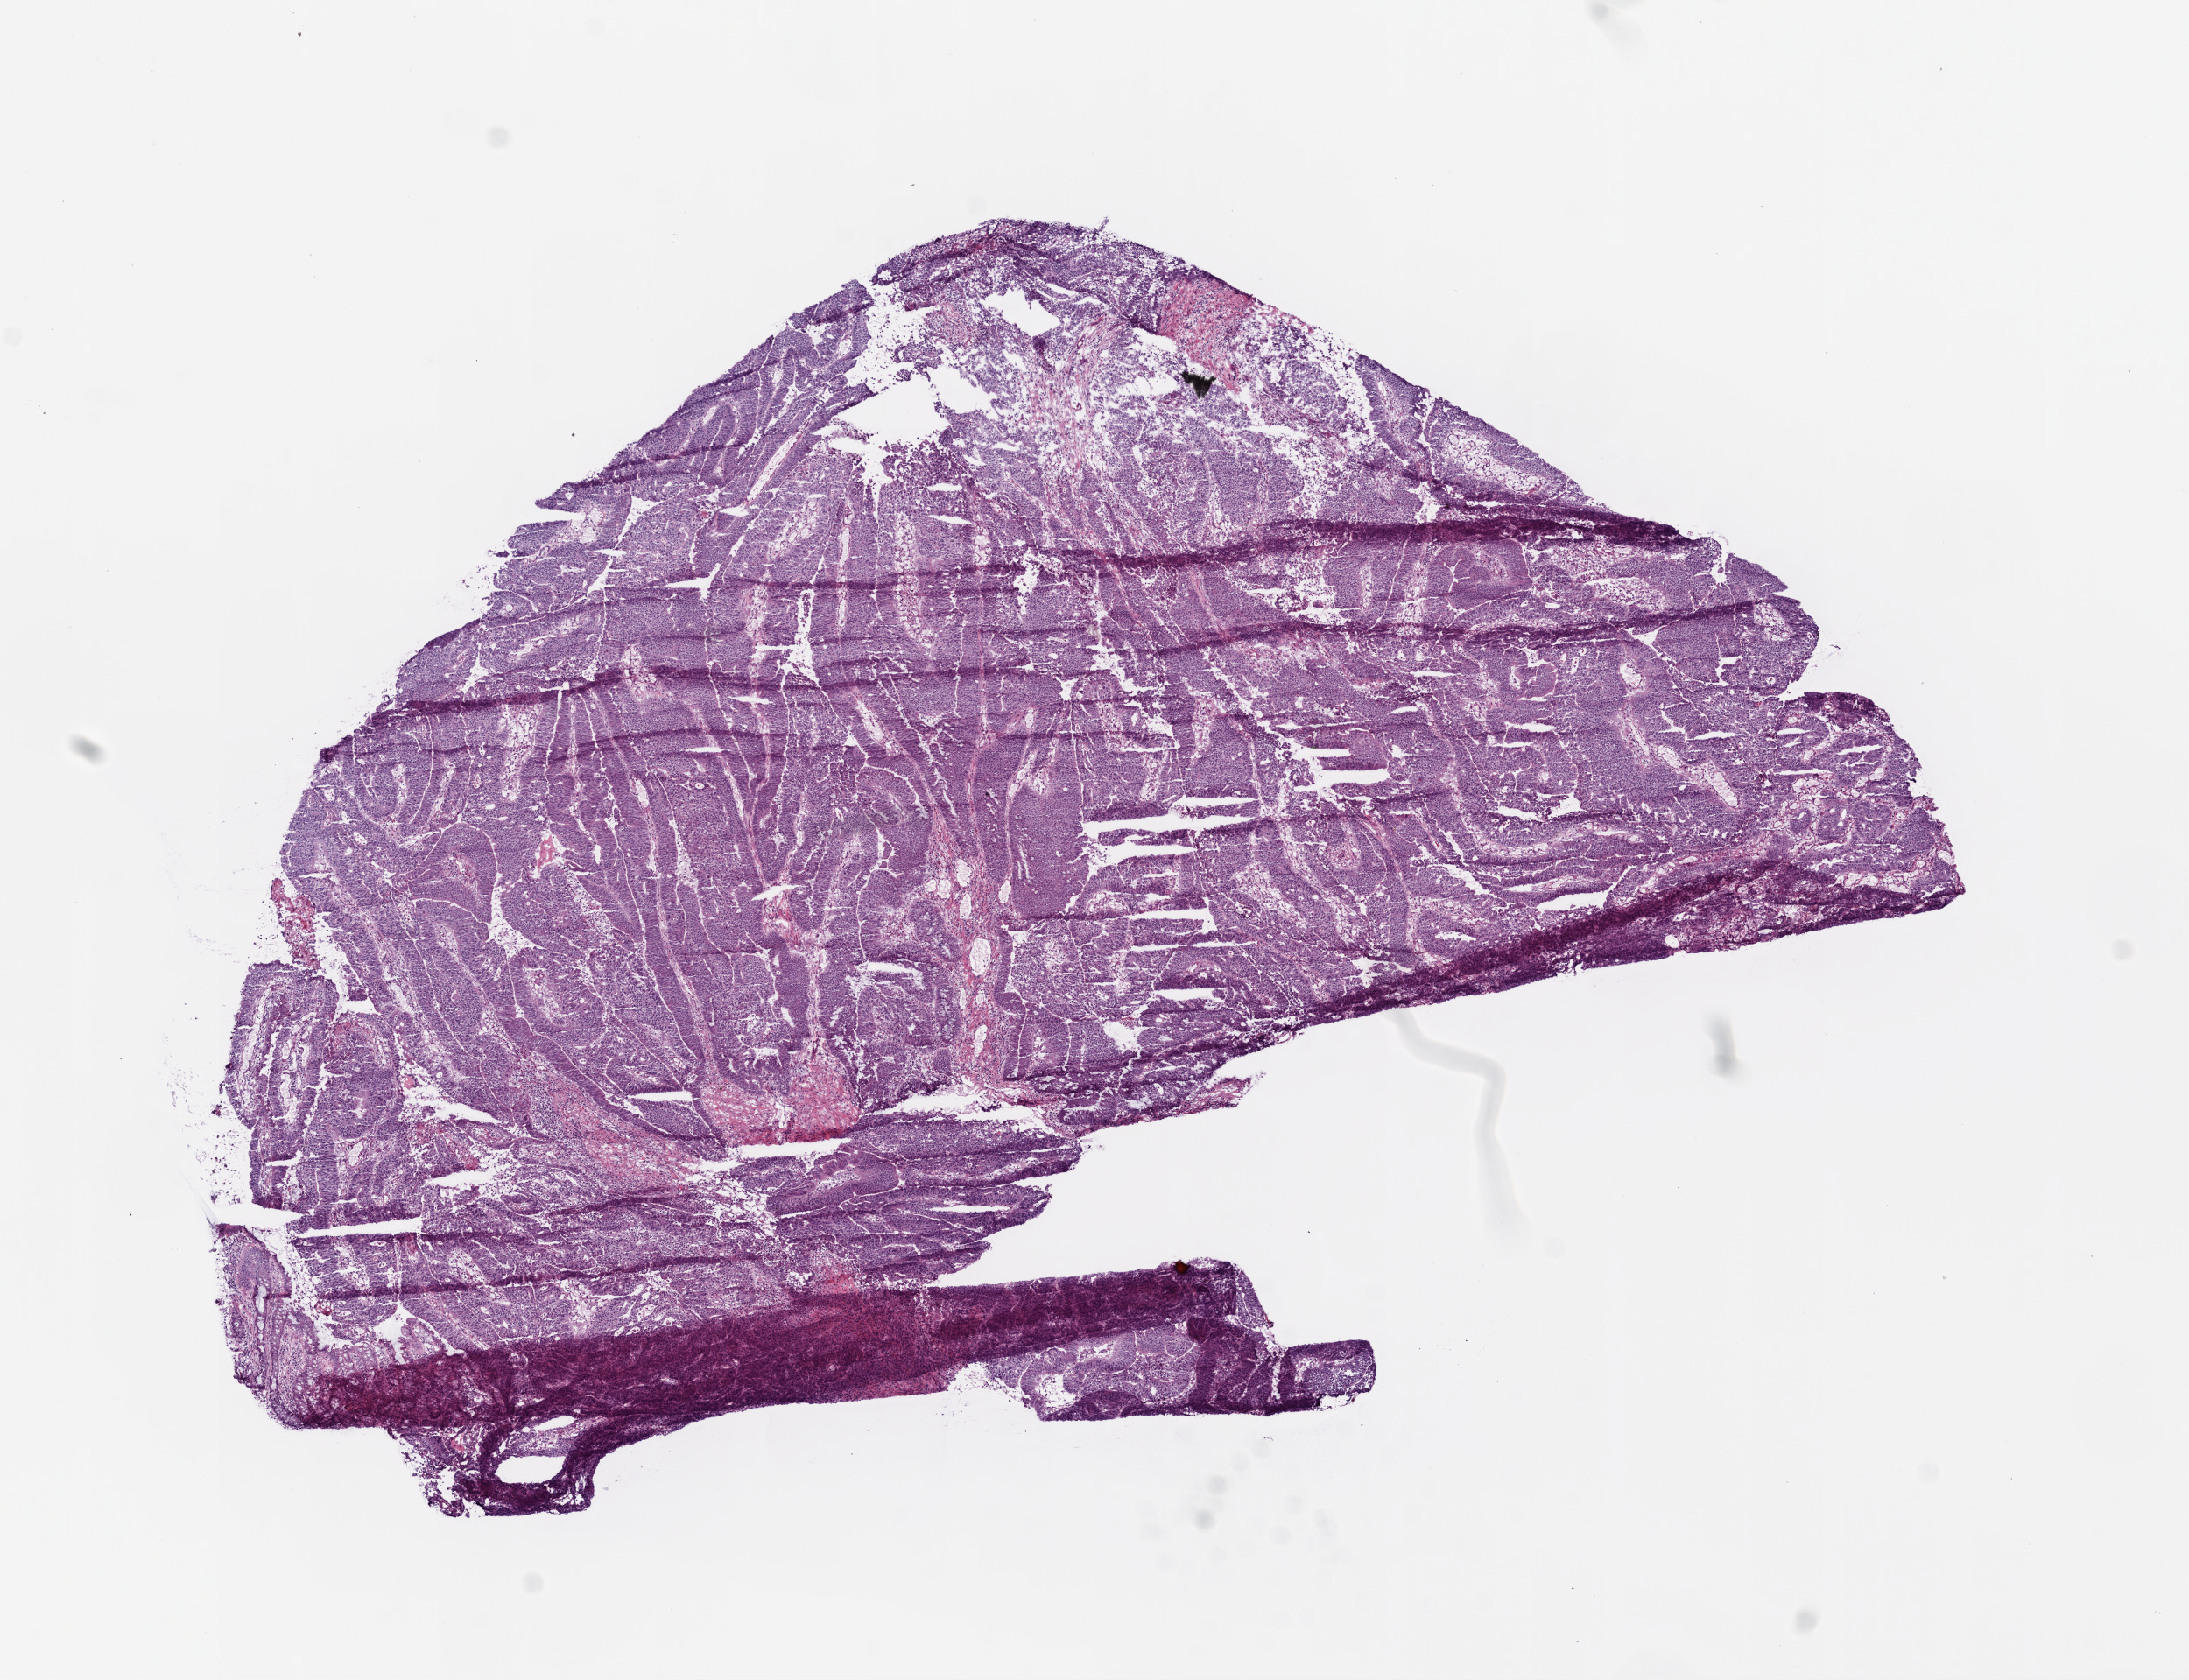
Whole-slide histology image, Hematoxylin and eosin (H&E) stained — whole scanned area (about 10.0 x 7.7 mm) shown as a low-resolution overview, frozen section from the top of the tissue portion, rectum, primary tumour sample. Male patient; age at initial diagnosis 69 years. Composition of this section per pathologist review: tumour cells 75%, tumour nuclei 75%, normal cells 20%, stromal cells 5%, necrosis 0%. Infiltration values recorded for this section: lymphocyte infiltration 50%, neutrophil infiltration 40%.
AJCC pathologic stage: IIA. Histologic diagnosis: Adenocarcinoma, NOS (rectosigmoid junction). Lymph nodes positive (case pathology): 0 of 65 examined.